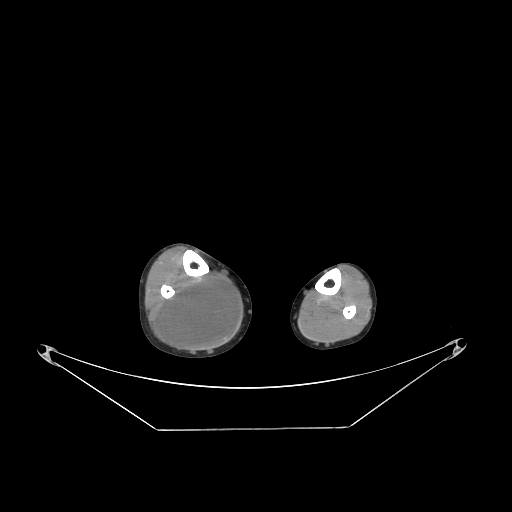
CT of an extremity soft-tissue mass (from a PET/CT study), one axial slice; slice 87 of 267 in the series (ordered by position); reconstruction kernel STANDARD; 140 kVp; soft-tissue window (W 400 / L 40 HU); 3.75 mm slice thickness; 512 × 512 image matrix, field of view 500 × 500 mm. Male patient. From the clinical record (not read from this slice): histological type: liposarcoma - round cell; grade: high; site of the primary tumour: right calf.
Outlined on this slice (expert contour drawn on MRI and transferred to this co-registered scan by the dataset authors):
- gross tumour volume (mass): box from (x=160, y=276) to (x=238, y=348) px